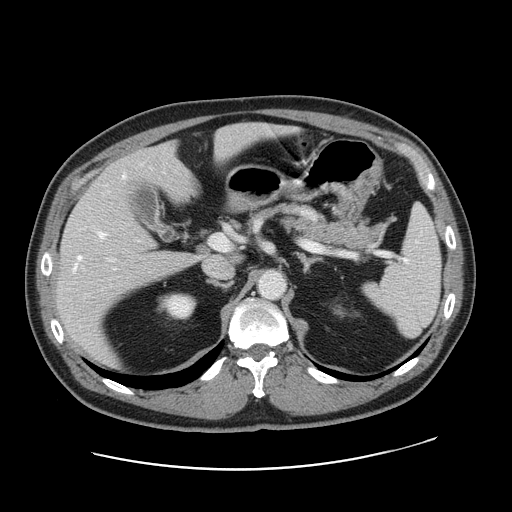
Contrast-enhanced abdominal CT, one axial slice. Slice 98 of 178 in the series (ordered by position). 120 kVp. Intravenous contrast given. Soft-tissue window (W 400 / L 40 HU). 2.5 mm slice thickness. 512 × 512 image matrix, field of view 403 × 403 mm. Male patient, age 63 years. Case-level facts recorded for this patient, not image findings: diagnosis: colorectal cancer liver metastases, imaged before liver resection; multiple liver metastases: yes.
Annotated regions visible in this slice (expert manual segmentation):
- hepatic veins: bounding box [x1, y1, x2, y2] px = [75, 175, 125, 269]
- liver: [57, 124, 284, 363]
- planned liver remnant (the part of the liver to remain after resection): [119, 124, 287, 202]
- portal vein (with intrahepatic branches): [109, 234, 229, 261]